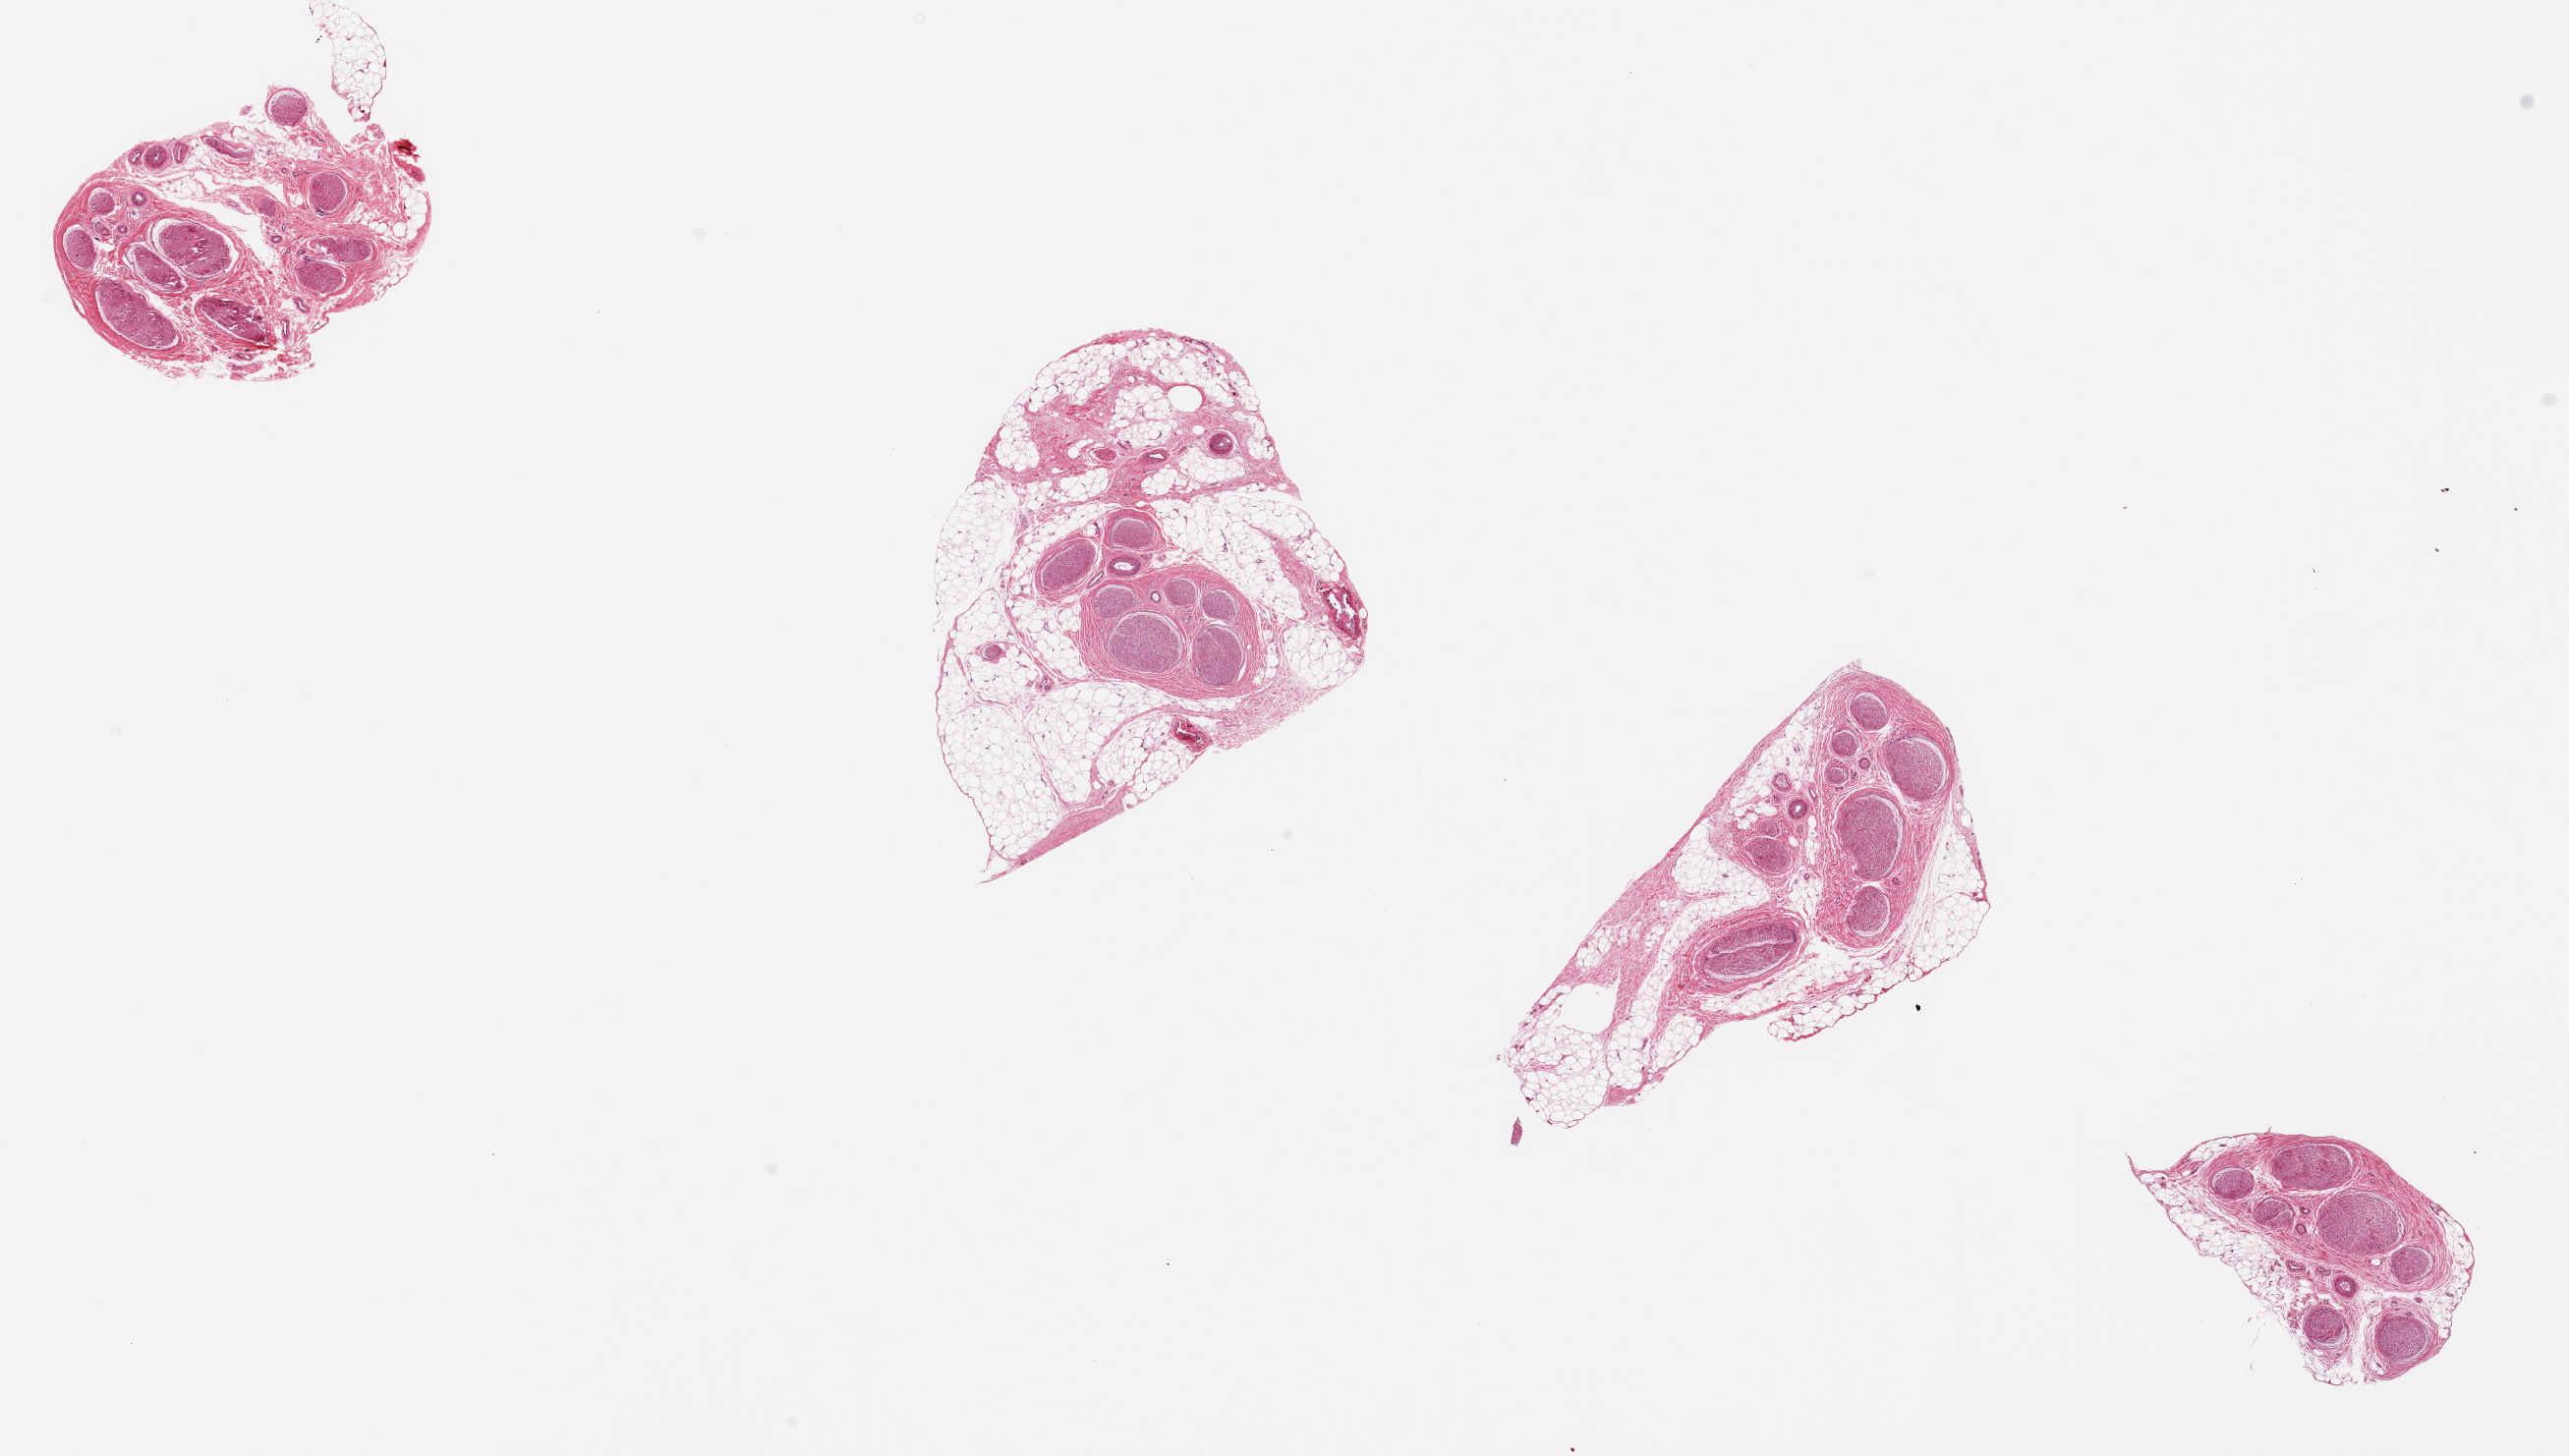
Whole-slide image, haematoxylin and eosin stain, shown as a low-resolution overview of the whole scanned area (about 20.7 x 11.7 mm, slide scanned at 20x), PAXgene-fixed, paraffin-embedded tissue, sampled site (target tissue): tibial nerve, tissue donor sample.
Reviewer comment on this tissue sample: 4 ~2-3mm d. pieces of nerve with ~1mm rim of fat/fibrous tissue.